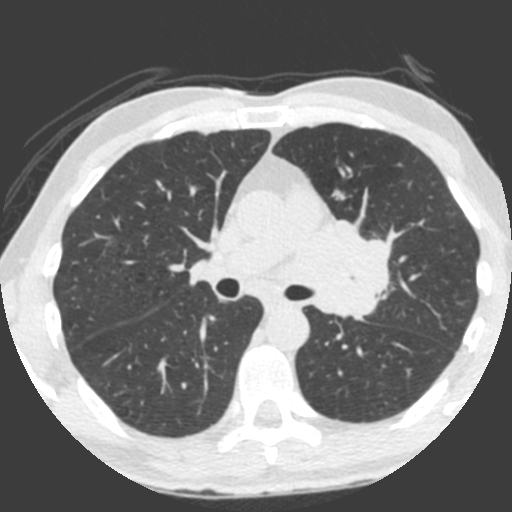
Axial slice from a low-dose chest CT screening exam; third screening round (two years after baseline); lung window (W 1500 / L -600 HU); 2 mm slice thickness; standard (soft-tissue) reconstruction kernel (B); slice 133 of 212 in the series; 512 × 512 image matrix. Male participant, aged 55 years at enrolment.
Expert-annotated lung lesion, bounding box [x1, y1, x2, y2] px = [309, 216, 399, 325]. Reader record for this screening exam (exam-level; its link to the box is not recorded): non-calcified nodule or mass ≥4 mm, left upper lobe, 49 × 29 mm, spiculated (stellate) margins, soft tissue attenuation, pre-existing on the prior screen: yes; interval growth: yes. Official screen result: positive, other. Participant outcome: lung cancer diagnosed 0 days after this screen — small cell carcinoma, NOS, left upper lobe, undifferentiated (G4), stage IV (AJCC 6th edition), 60 mm at pathology.